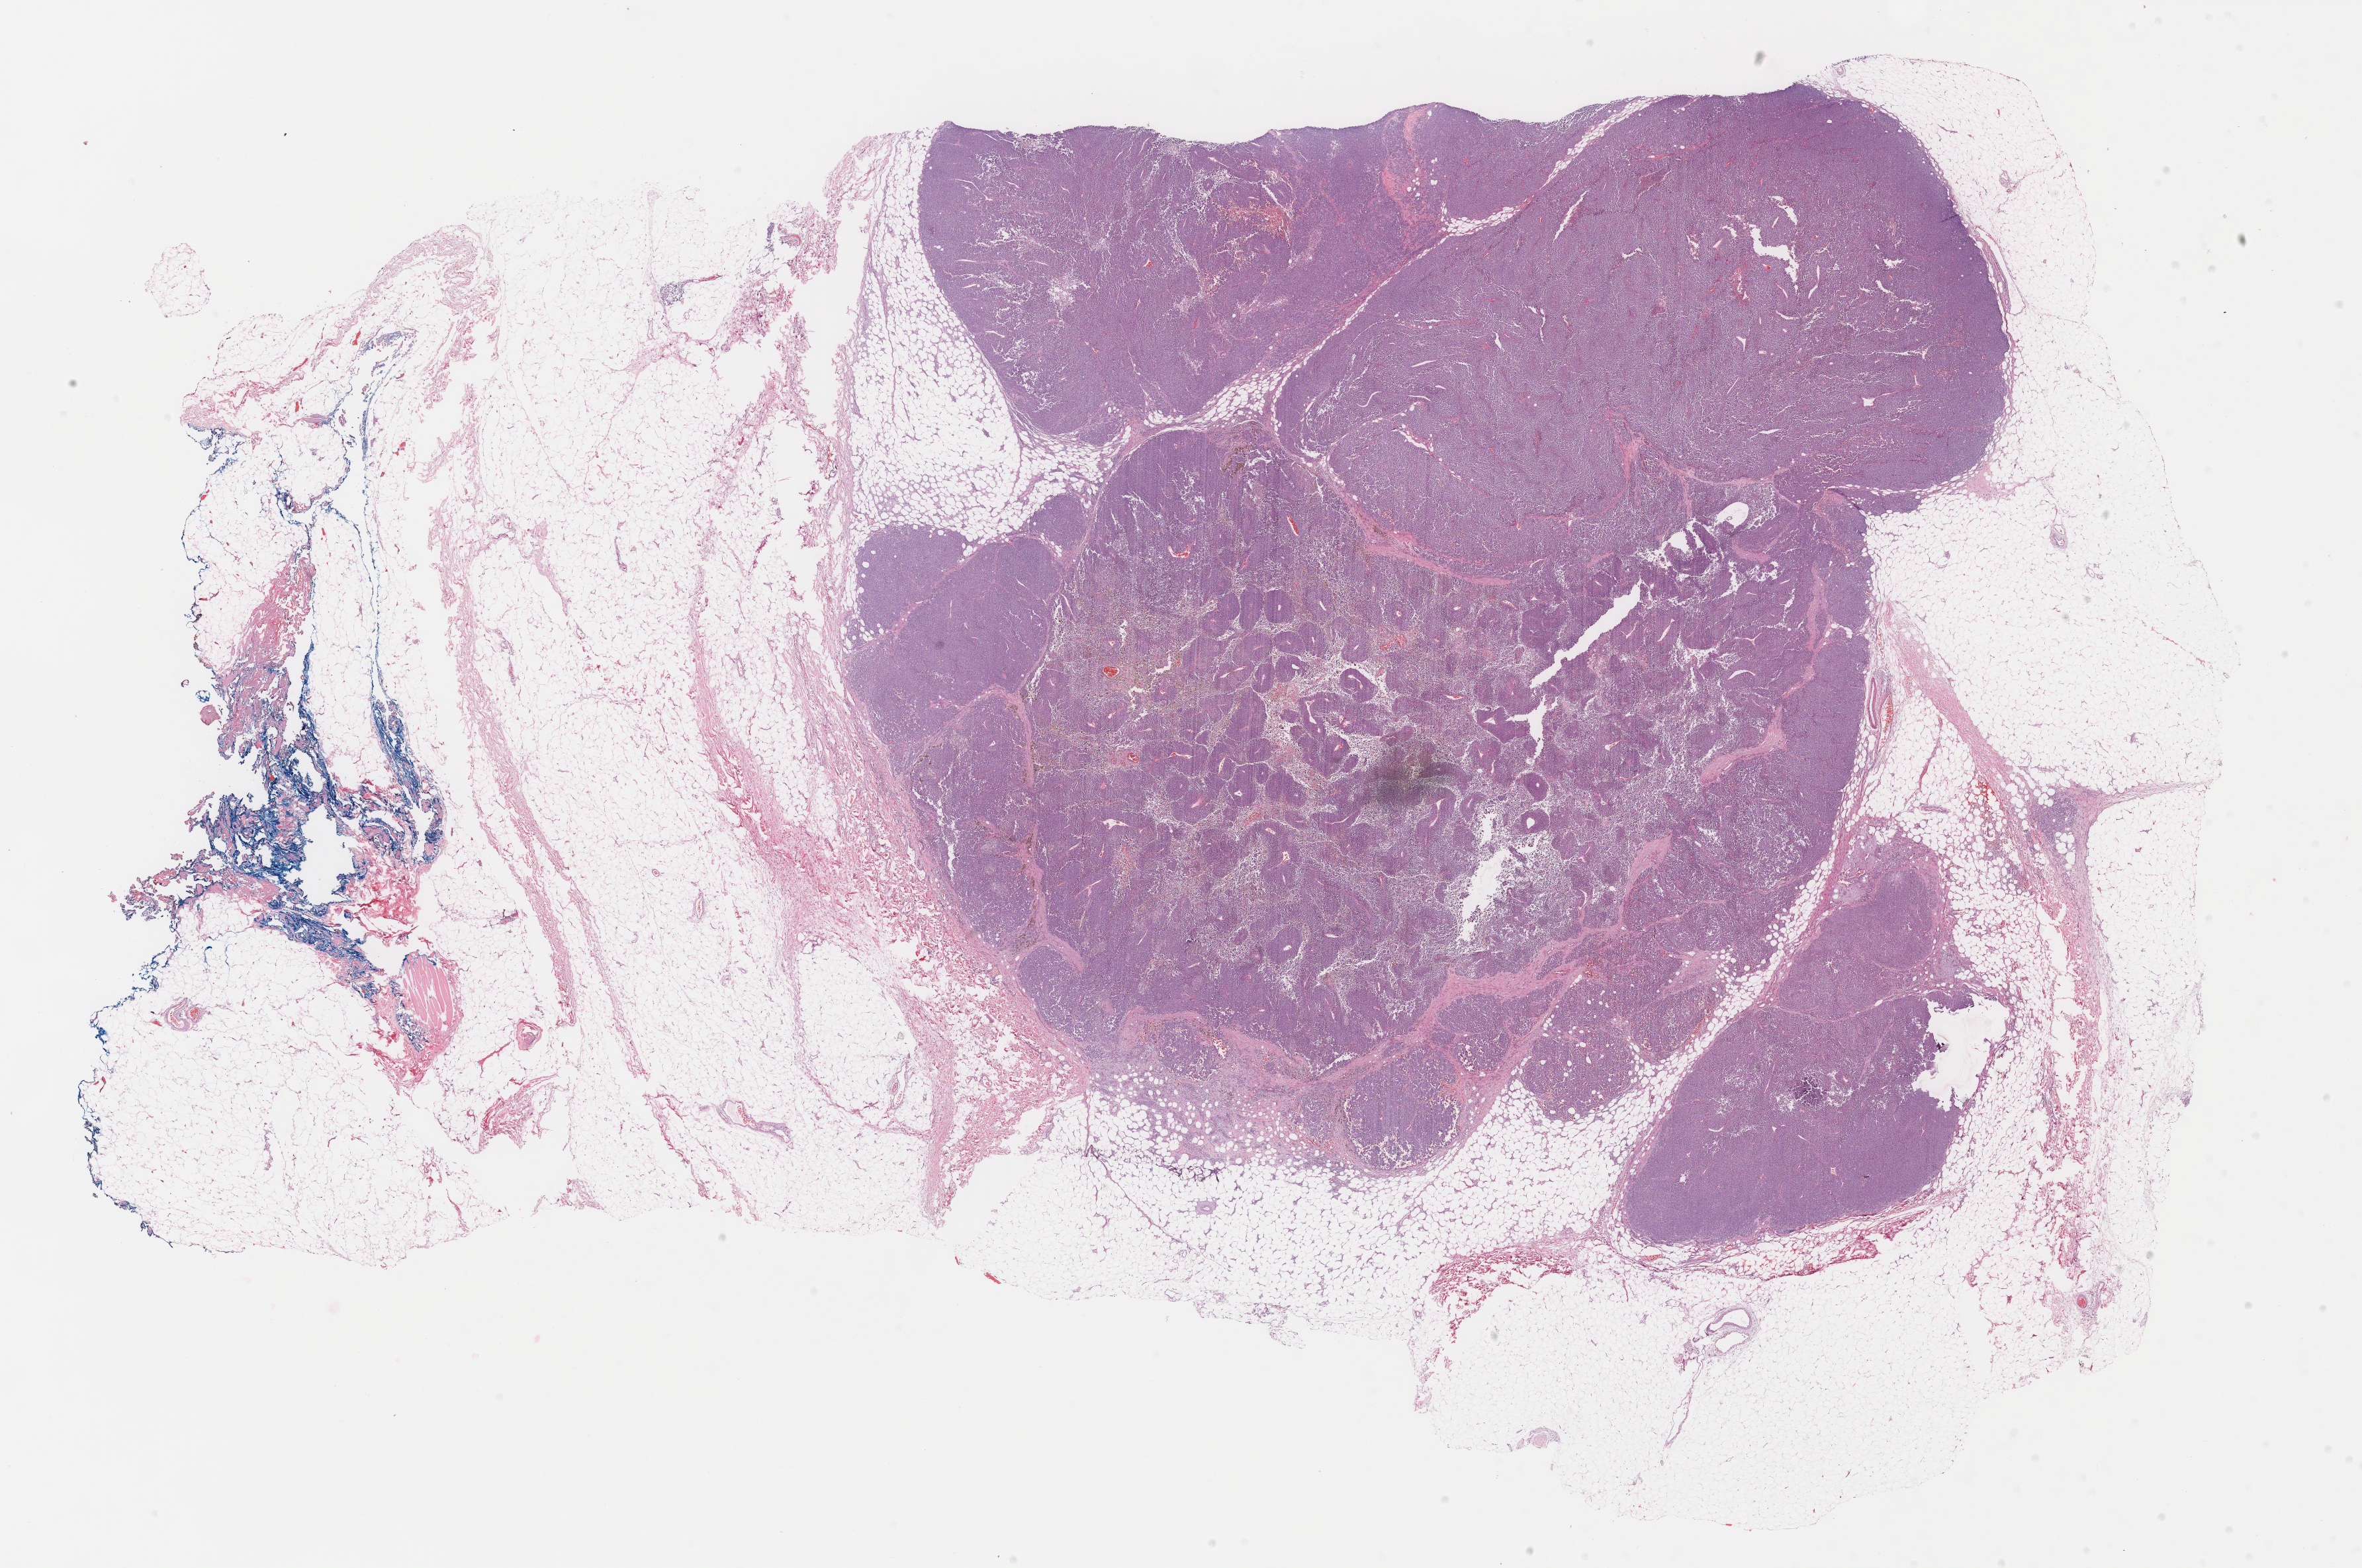
Digitized H&E-stained tissue section (whole slide) — shown as a low-resolution overview of the whole scanned area (about 28.3 x 18.8 mm); formalin-fixed paraffin-embedded (FFPE) diagnostic section; primary tumour sample from the skin. Patient: female, age at initial diagnosis 47 years.
Histologic diagnosis: Malignant melanoma, NOS.